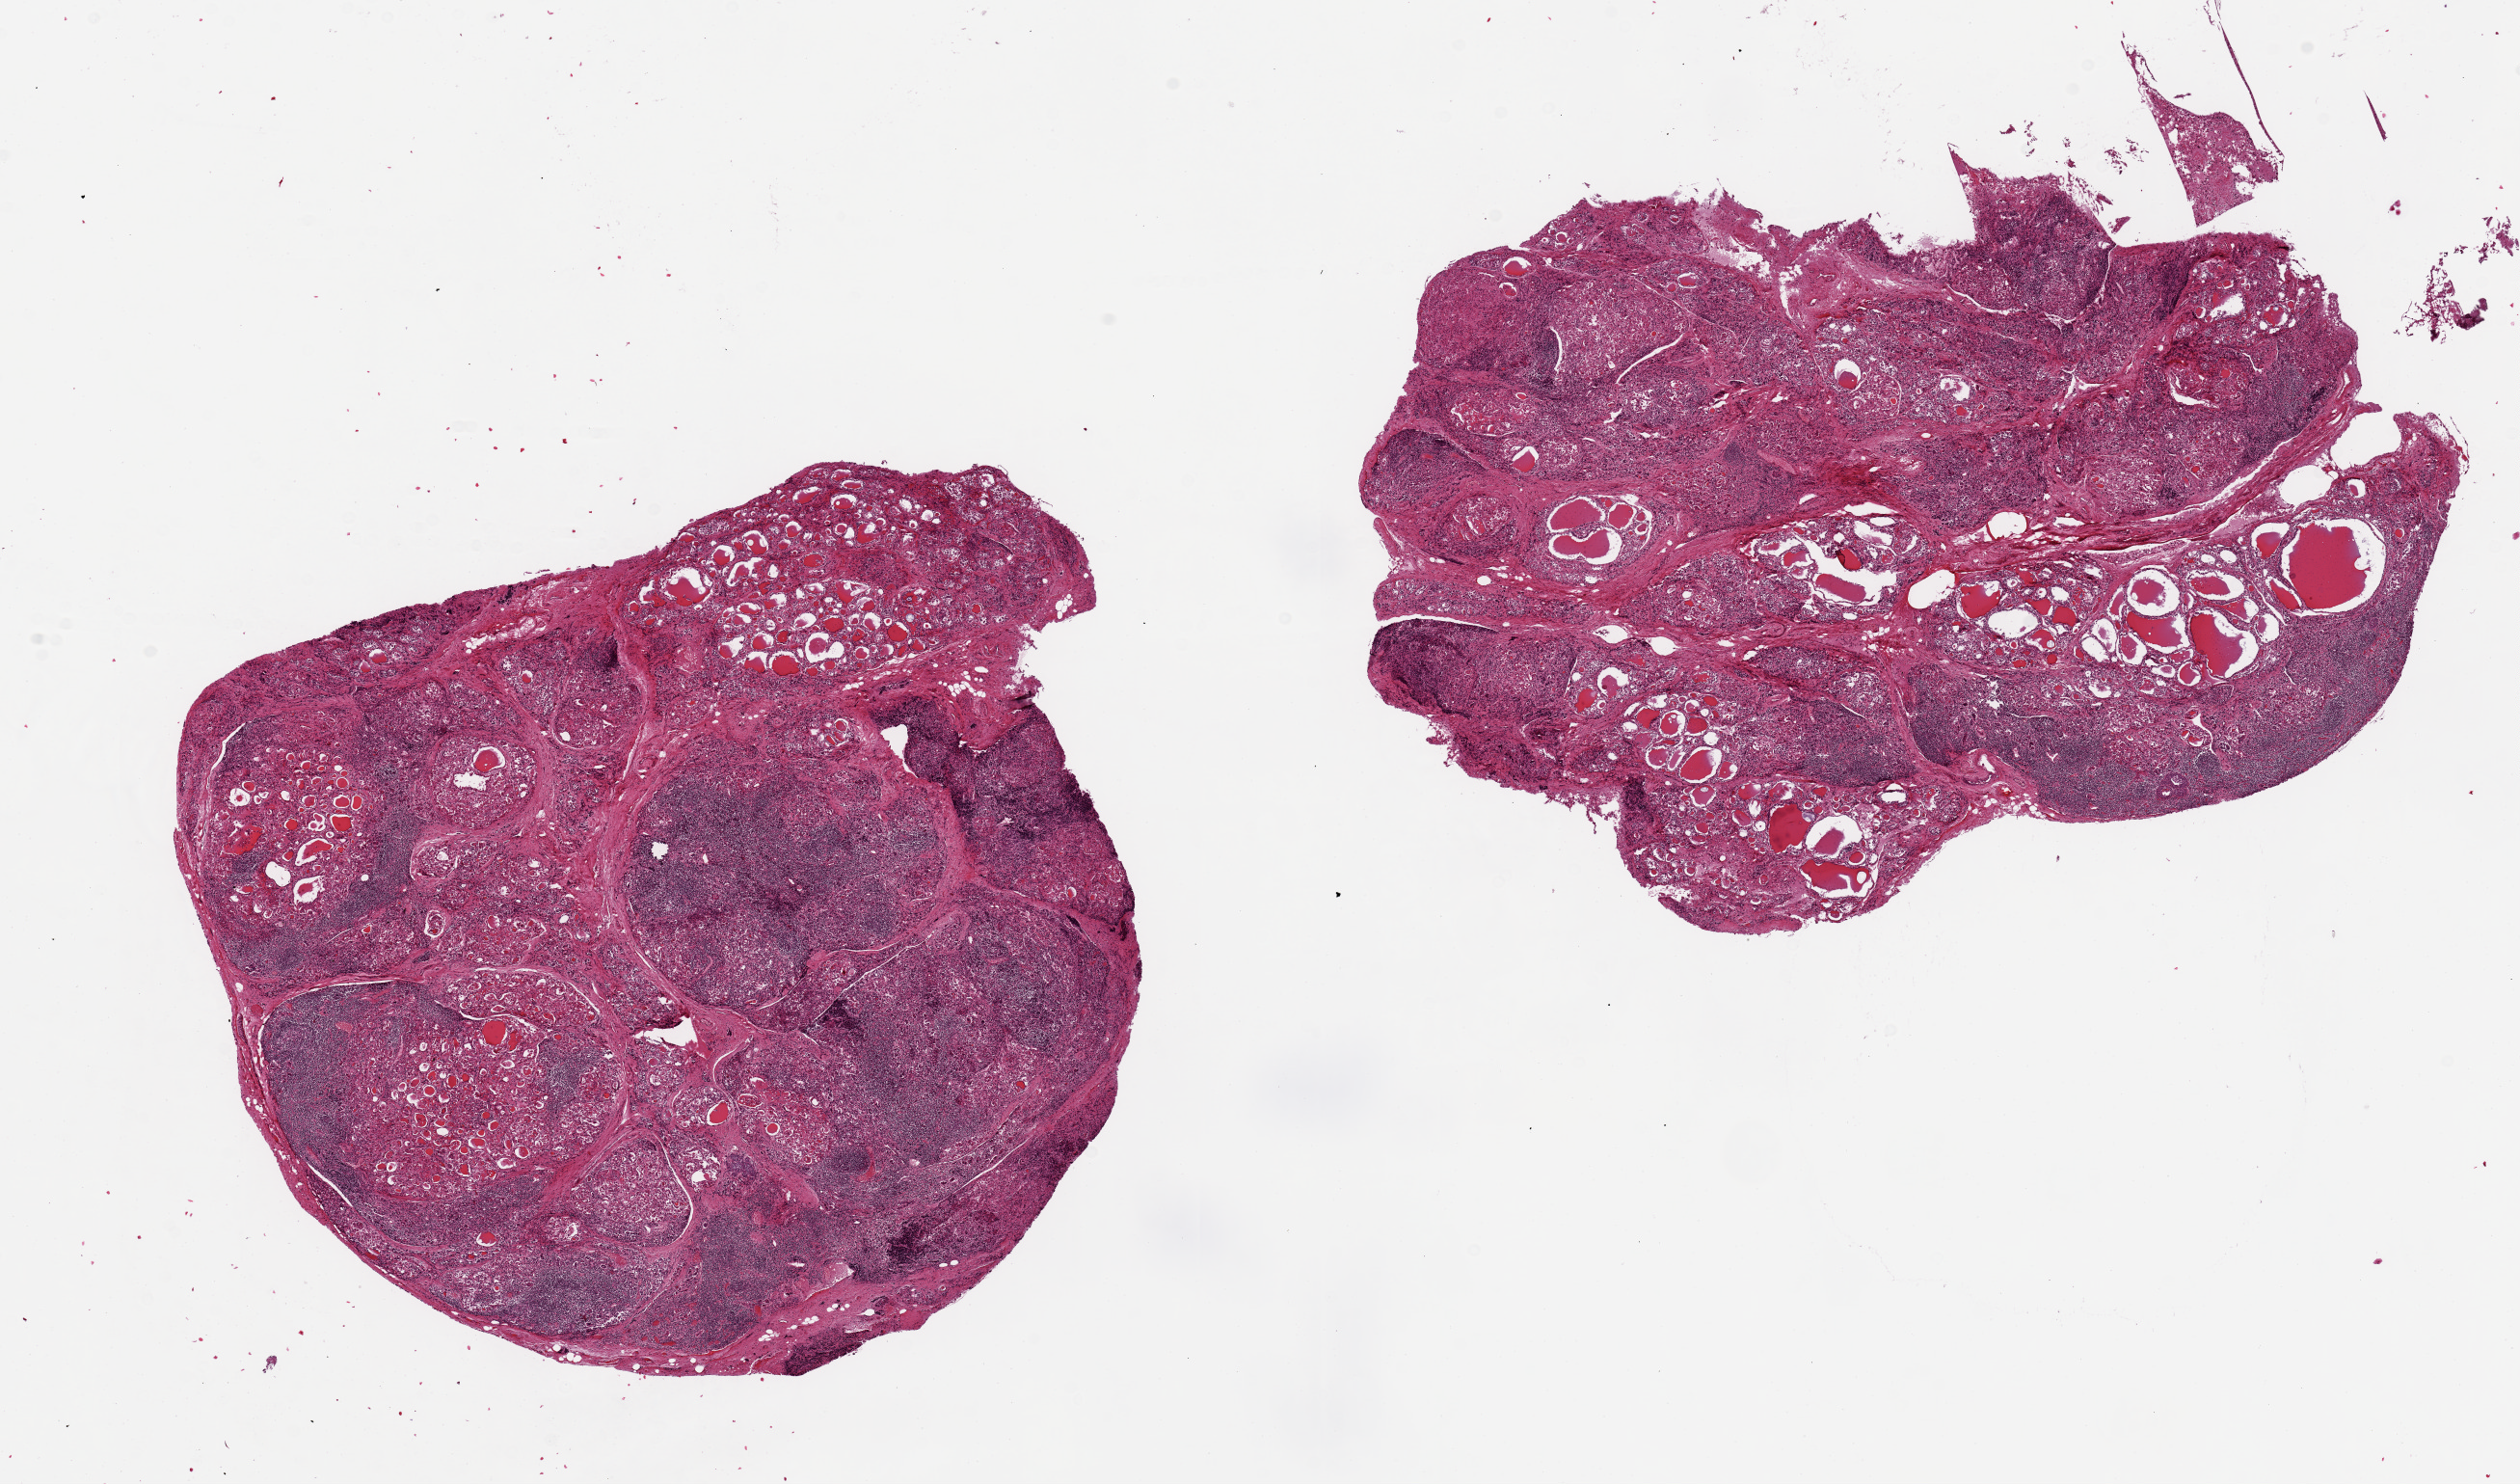
Digitized H&E-stained section, brightfield, whole scanned area (about 20.7 x 12.2 mm, slide scanned at 20x) shown as a low-resolution overview, PAXgene-fixed, paraffin-embedded tissue, section of thyroid (target tissue), tissue donor sample. Donor sex: male.
- review note (as recorded): 2 pieces, 8x7 & 10x8mm; Hashimoto's thyroiditis with regressive features/fibrosis